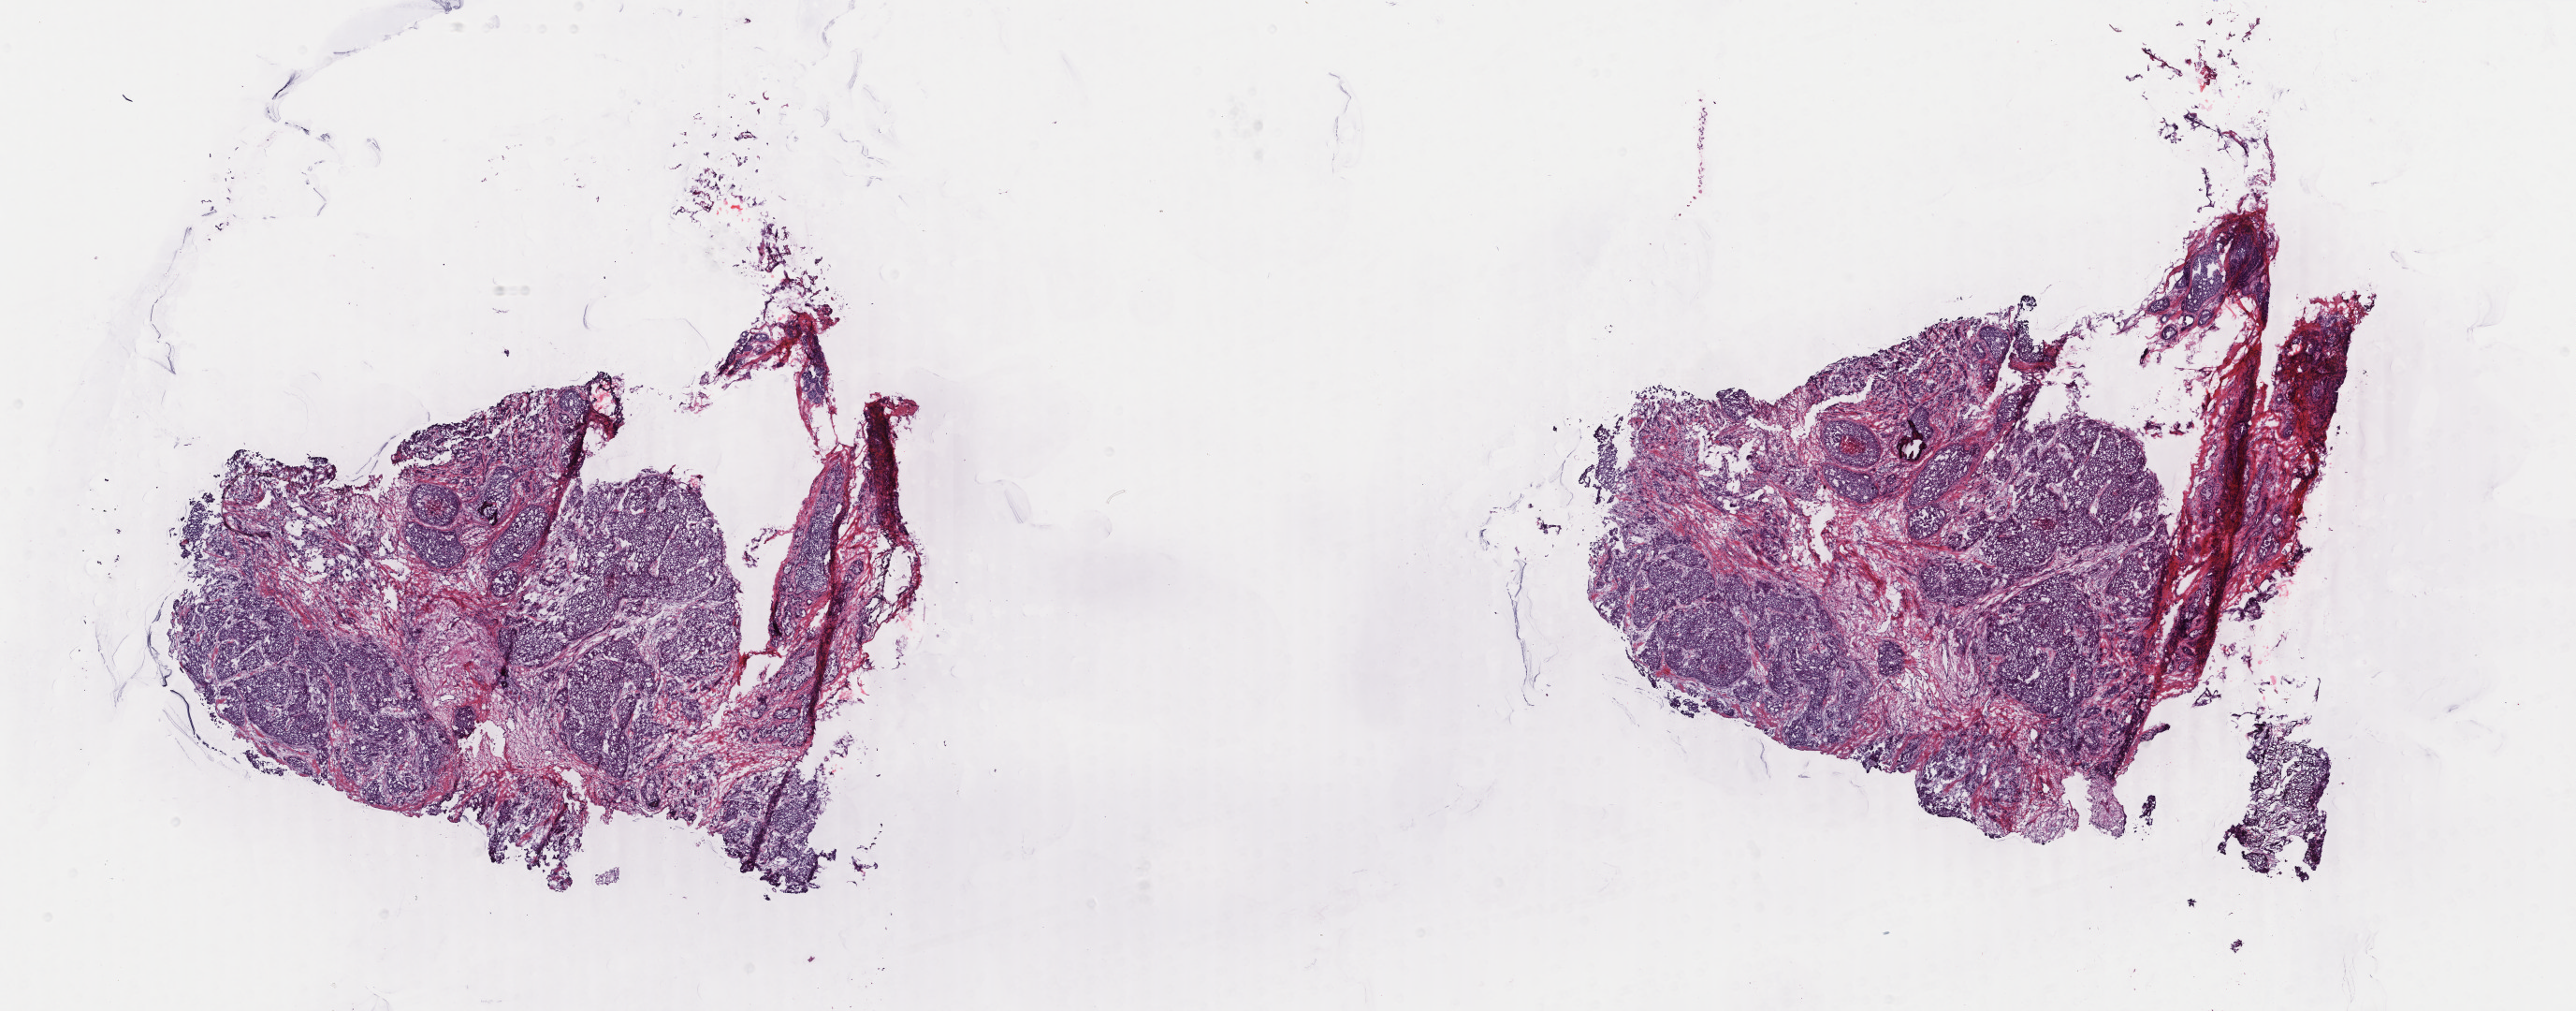
H&E whole-slide image — a low-resolution overview of the entire scanned area, about 21.9 x 8.6 mm, frozen section, breast, primary tumour sample. Female patient; age at initial diagnosis 37 years. Slide review estimates, as recorded: tumour cells 60%, tumour nuclei 65%, normal cells 5%, stromal cells 35%, necrosis 0%. Inflammatory infiltration, as recorded: lymphocyte infiltration 1%, monocyte infiltration 0%, neutrophil infiltration 0%.
- AJCC pathologic stage: IIA
- histologic diagnosis: Infiltrating duct carcinoma, NOS
- laterality: left